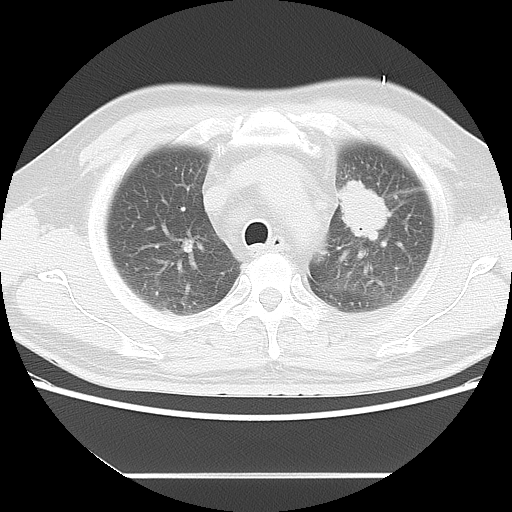
Chest CT, one axial slice; slice 8 of 14 in the series (ordered by position); reconstruction kernel LUNG; 120 kVp; lung window (W 1500 / L -600 HU); 512 × 512 image matrix, field of view 350 × 350 mm. Male patient, age 56 years. Case-level facts recorded for this patient, not image findings: clinical TNM (as recorded): T2 N3 M1.
Outlined on this slice (bounding box drawn by a radiologist):
- lung tumour (recorded histology: adenocarcinoma): bounding box [x1, y1, x2, y2] px = [332, 177, 399, 246]